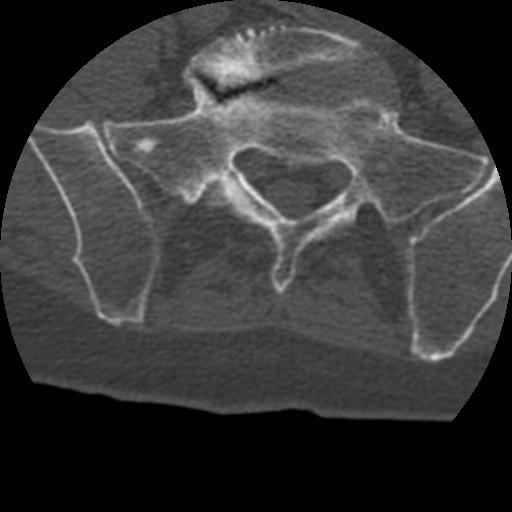
CT including the spine, one axial slice. Position 28 of 399 along the scan axis. Reconstruction kernel STANDARD. 120 kVp. Bone window (W 1800 / L 400 HU). 1.25 mm slice thickness. 512 × 512 image matrix, field of view 160 × 160 mm. Patient age 69 years. From the clinical record (not read from this slice): primary cancer: prostate.
Outlined on this slice (semi-automatically segmented with operator editing):
- L5 vertebra: bounding box [x1, y1, x2, y2] px = [190, 25, 375, 207]